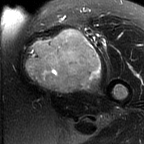
MRI of an extremity soft-tissue mass, one axial slice. Position 43 of 60 along the scan axis. T2-weighted fat-saturated. MR volume resampled by the dataset authors to the PET/CT grid (not the native acquisition matrix). 3.27 mm slice thickness. 144 × 144 image matrix. Female patient. Case-level facts recorded for this patient, not image findings: histological type: pleiomorphic leiomyosarcoma; grade: intermediate; site of the primary tumour: left thigh.
Outlined on this slice (expert contour drawn on MRI and transferred to this co-registered scan by the dataset authors):
- gross tumour volume including surrounding oedema: bounding box <25,28,101,93> (left, top, right, bottom; pixels)
- gross tumour volume (mass): <25,28,101,93>